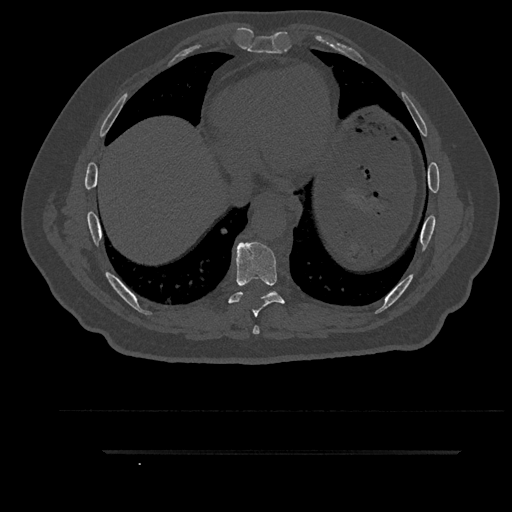
CT including the spine, one axial slice; slice 473 of 797 in the series (ordered by position); reconstruction kernel Br40s/3; 120 kVp; bone window (W 1800 / L 400 HU); 0.5 mm slice thickness; 512 × 512 image matrix. Male patient, age 63 years. Case-level facts recorded for this patient, not image findings: primary cancer: renal.
Outlined on this slice (semi-automatic segmentation, software-assisted and operator-edited):
- T7 vertebra: bounding box (x1, y1, x2, y2) in pixels: (252, 326, 260, 335)
- T8 vertebra: (228, 242, 292, 317)